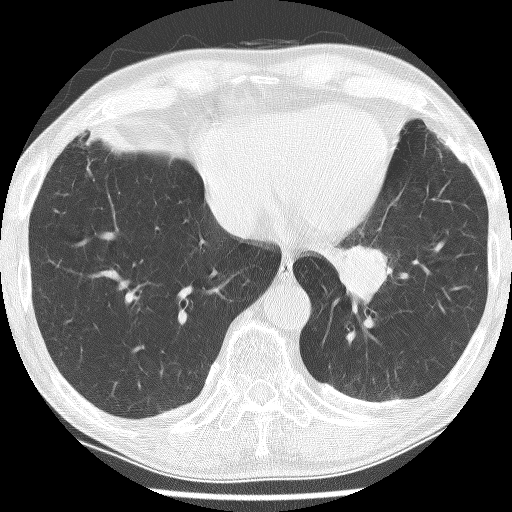
Chest CT (low-dose screening protocol), one axial image. Baseline screening round. Lung window (W 1500 / L -600 HU). Slice 177 of 226 in the series. Male, age 74 years at enrolment. Current smoker at enrolment.
• Lesion marked by an expert reader, bounding box [x1, y1, x2, y2] px = [315, 222, 418, 315].
• Screening reader's record for this exam (one nodule recorded; not confirmed to be the boxed lesion): non-calcified nodule or mass ≥4 mm, left lower lobe, 30 × 27 mm, spiculated (stellate) margins, soft tissue attenuation.
• Participant outcome: lung cancer diagnosed 151 days after this screen — adenocarcinoma, NOS, left lower lobe, stage IIIA (AJCC 6th edition), 49 mm at pathology.